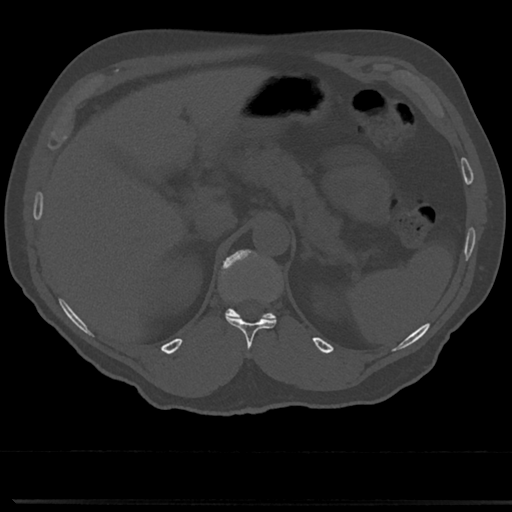
CT including the spine, one axial slice. Position 179 of 817 along the scan axis. 120 kVp. Bone window (W 1800 / L 400 HU). 0.5 mm slice thickness. 512 × 512 image matrix. Patient: male, 61 years. From the clinical record (not read from this slice): primary cancer: prostate.
Annotated regions visible in this slice (semi-automatic segmentation, software-assisted and operator-edited):
- T11 vertebra: bounding box (x1, y1, x2, y2) in pixels: (226, 317, 276, 353)
- T12 vertebra: (219, 249, 276, 321)